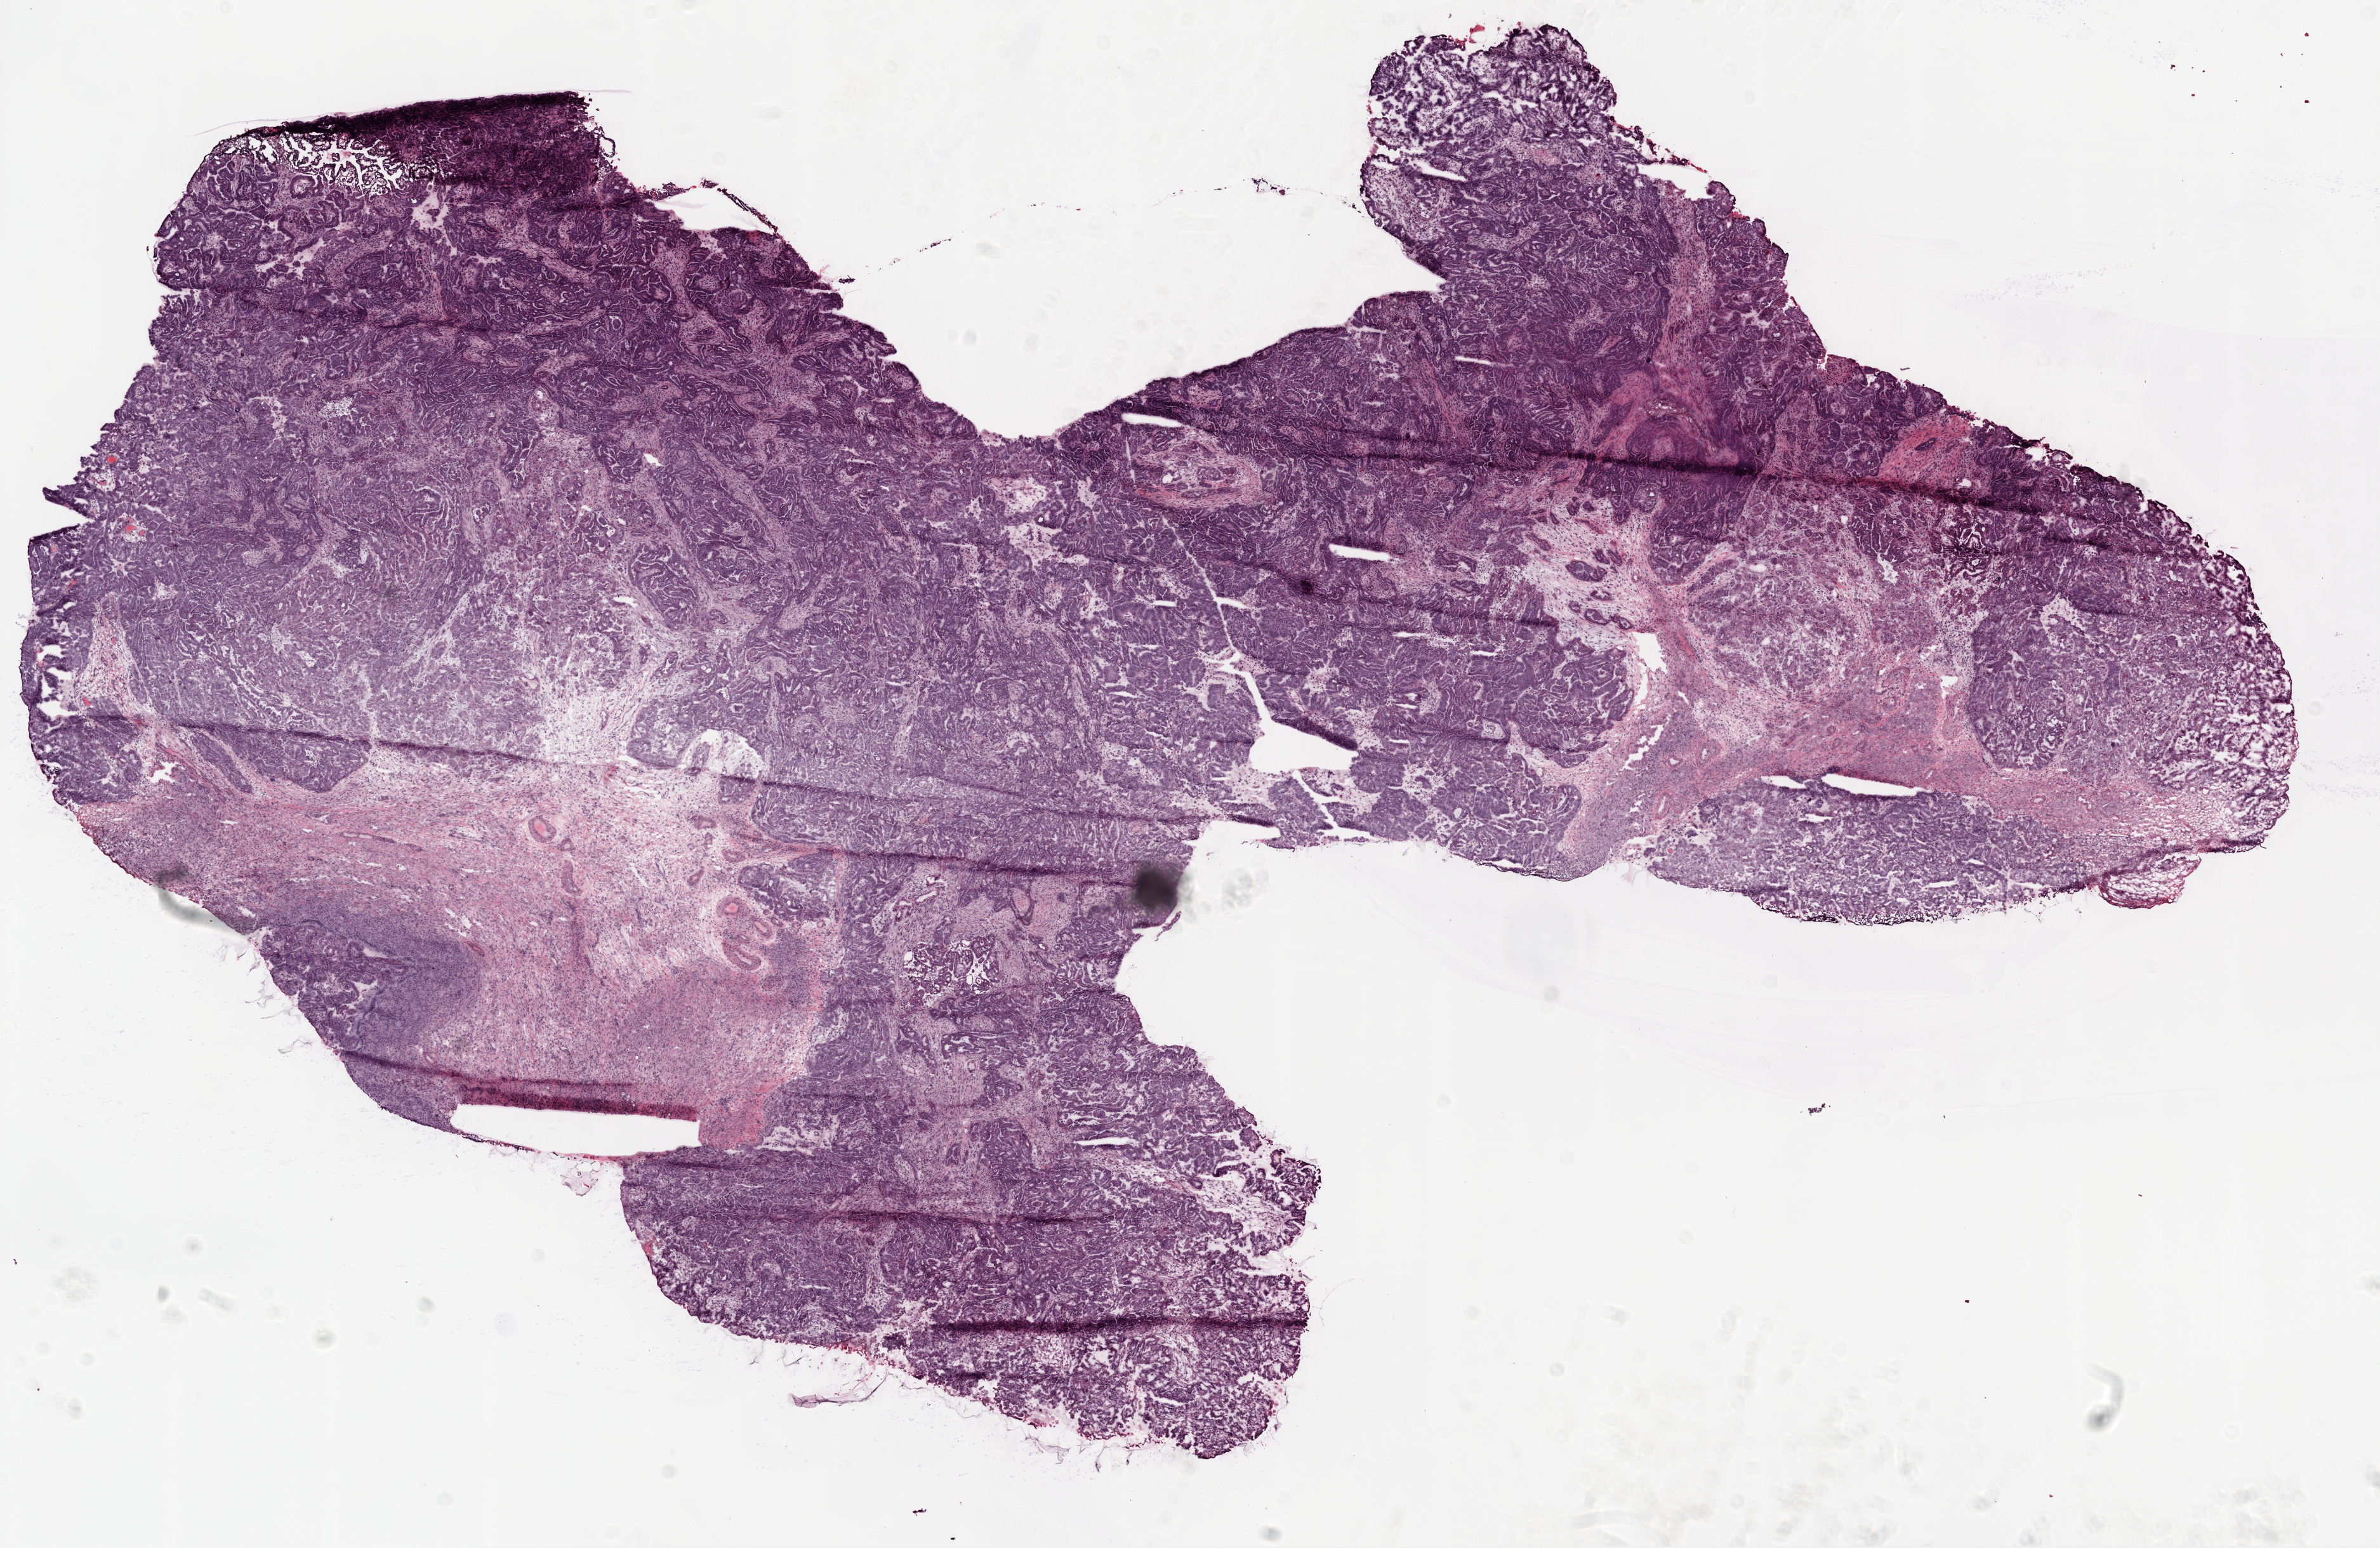
Whole-slide histology image, Hematoxylin and eosin (H&E) stained, a low-resolution overview of the entire scanned area, about 15.0 x 9.8 mm (acquisition: 20x scan); frozen section from the top of the tissue portion; primary tumour sample from the ovary. Female patient; age at initial diagnosis 45 years. Pathologist review of this section (percent, as recorded): tumour cells 85%, tumour nuclei 85%.
Pathologic diagnosis: Serous cystadenocarcinoma, NOS.